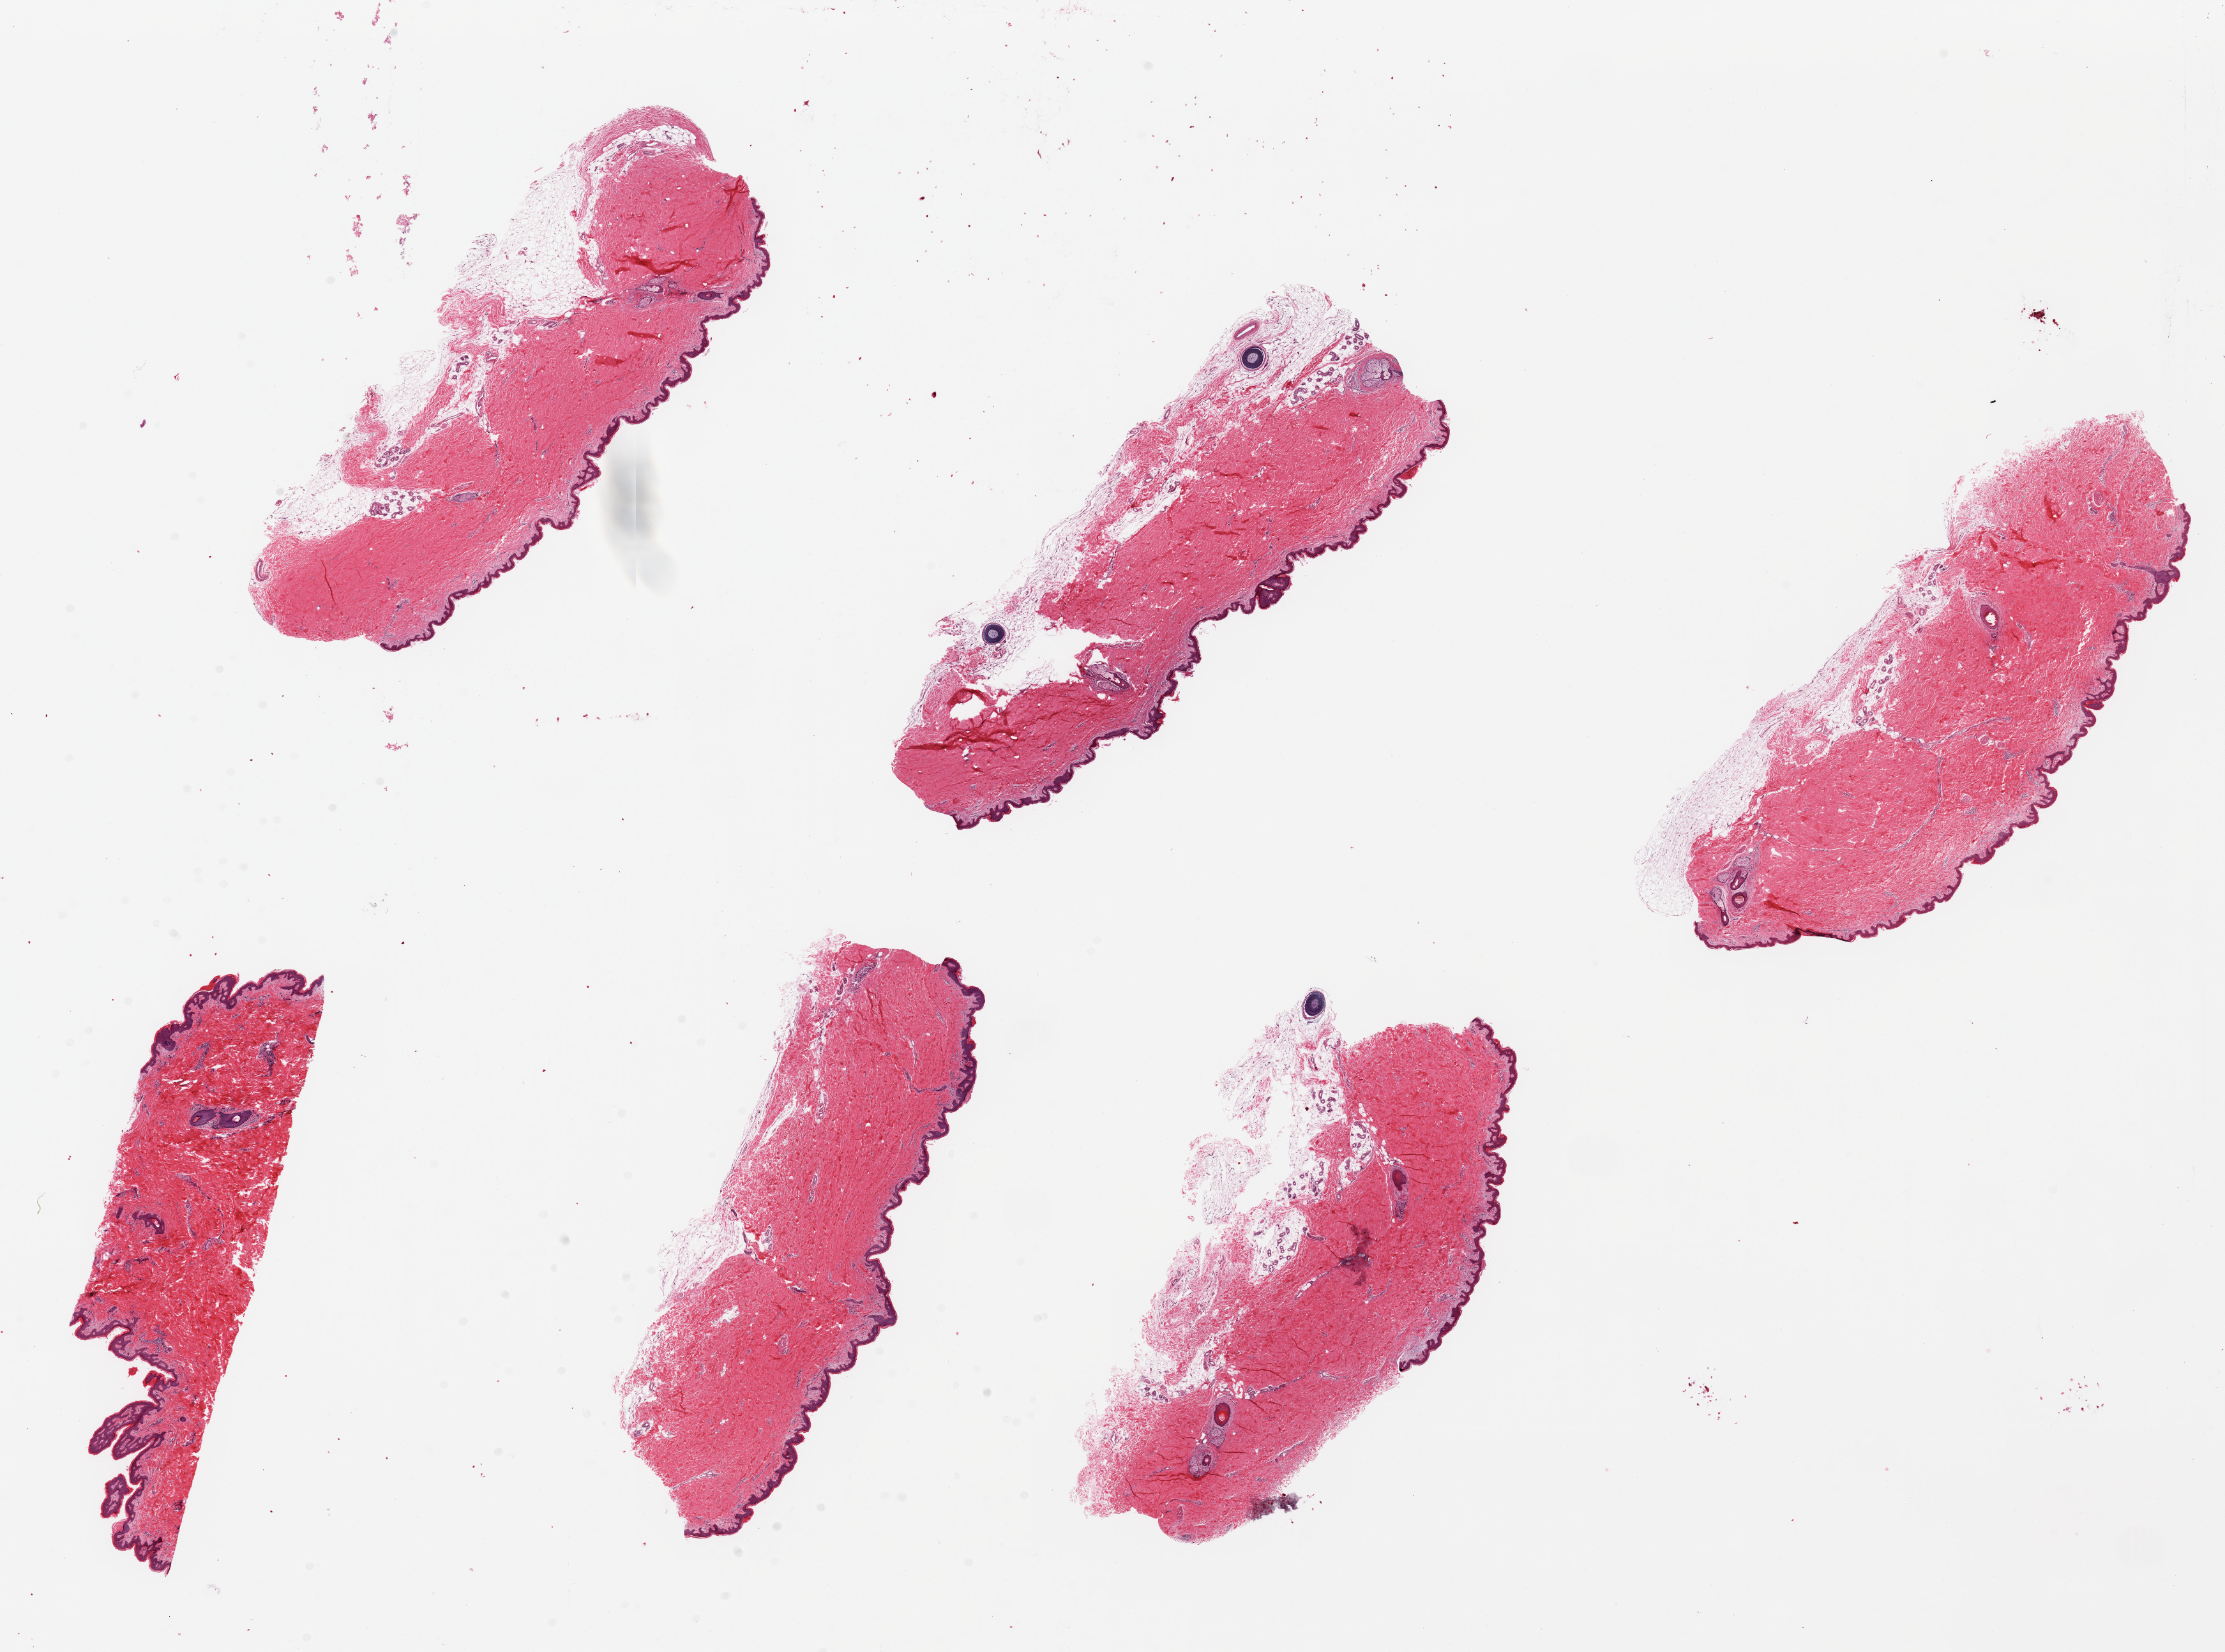
Digitized haematoxylin and eosin-stained section, a low-resolution overview of the entire scanned area, about 27.6 x 20.5 mm. PAXgene-fixed, paraffin-embedded tissue. Section of skin of suprapubic region (target tissue). Donor tissue sample. Male donor.
Review note (as recorded): 6 pieces, up to 8x3mm; squamous epitheium is ~1% thickness.